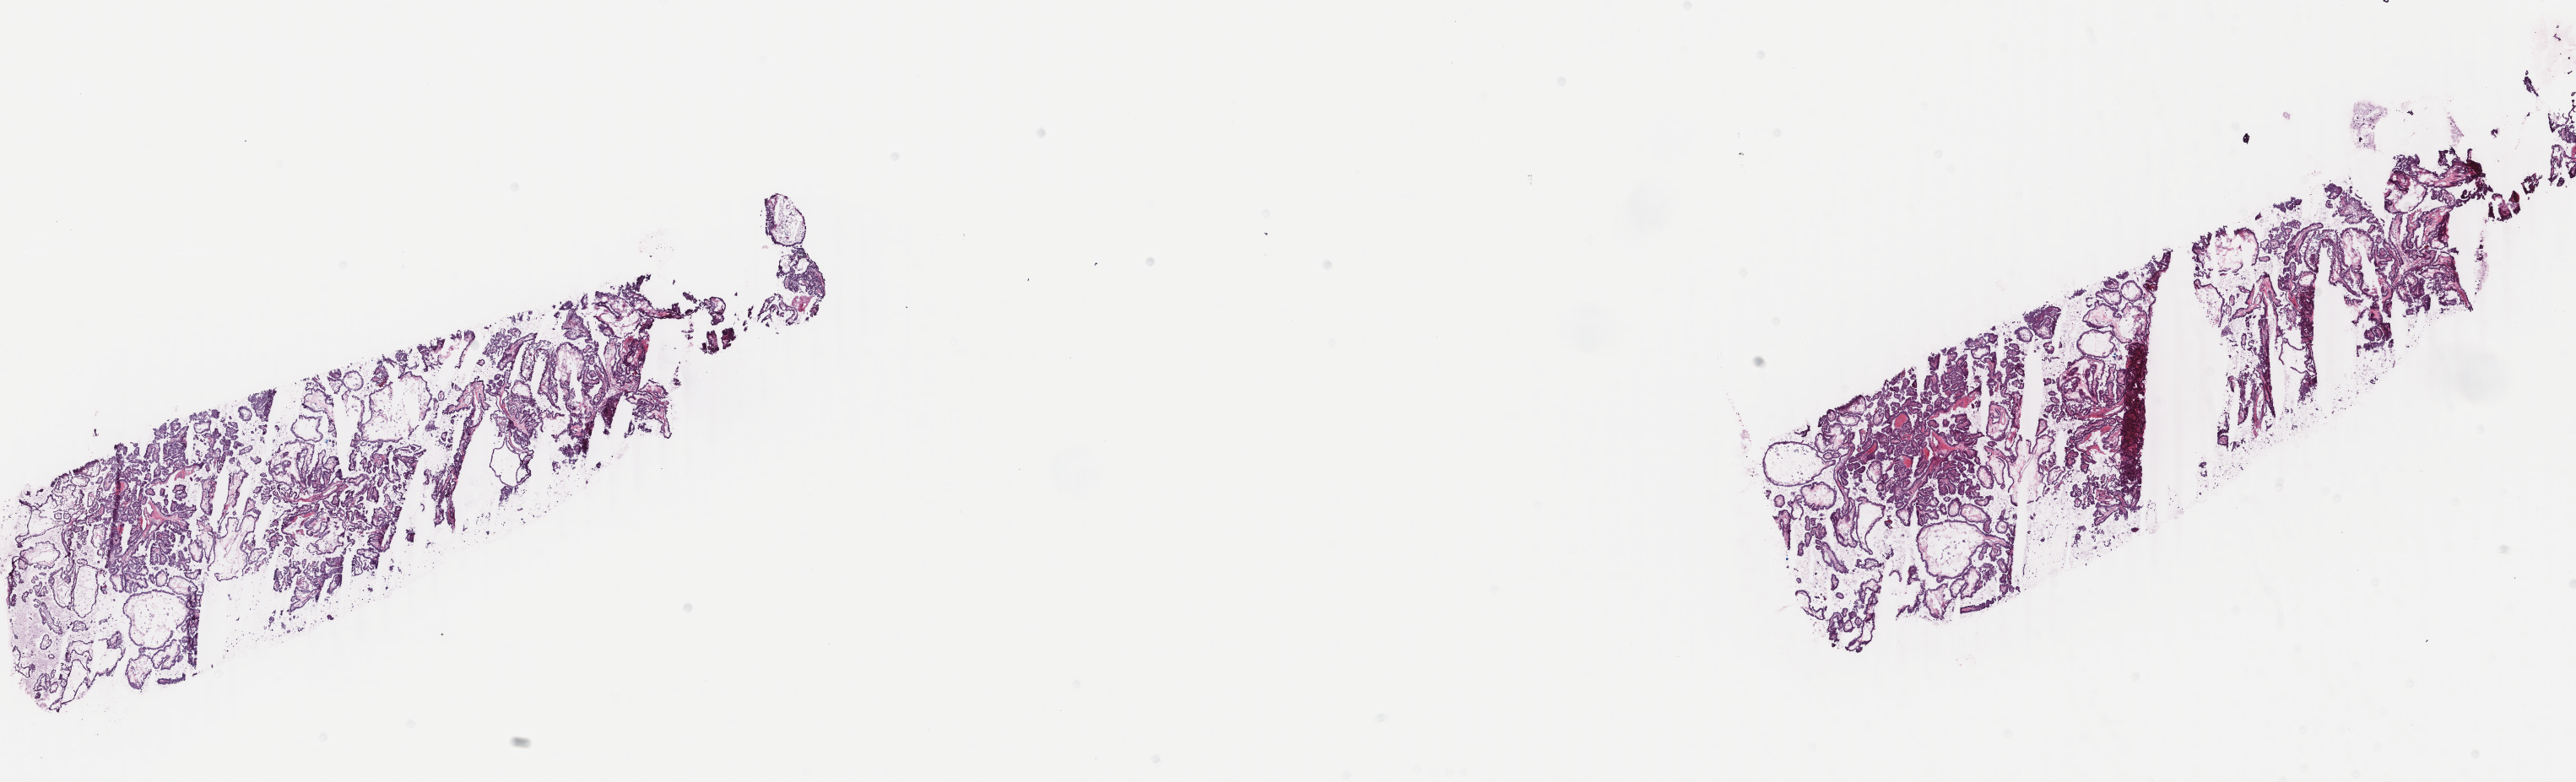
Hematoxylin and eosin (H&E) stained whole-slide image — a low-resolution overview of the entire scanned area, about 24.3 x 7.4 mm (from a 40x scan). Frozen section from the top of the tissue portion. Primary tumour sample from the thyroid. Female, age 30 years at initial diagnosis. Pathologist review of this section (percent, as recorded): tumour cells 99%, tumour nuclei 99%, normal cells 0%, stromal cells 1%, necrosis 0%. Infiltration values recorded for this section: lymphocyte infiltration 0%, monocyte infiltration 0%, neutrophil infiltration 0%.
Pathologic diagnosis: Papillary adenocarcinoma, NOS (thyroid gland). AJCC pathologic stage: I (7th edition). Lymph nodes positive (case pathology): 6 of 11 examined.